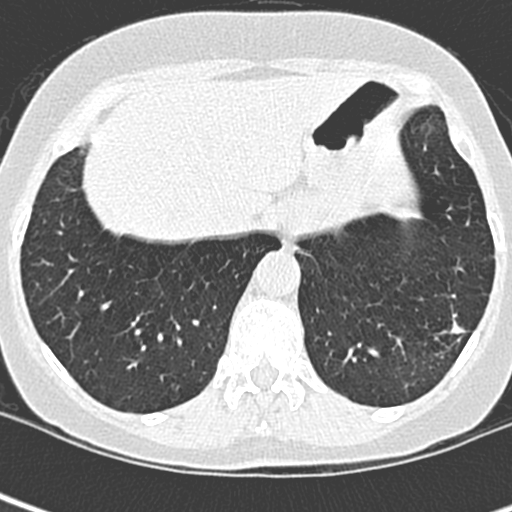
Low-dose screening chest CT, one axial slice. Position 62 of 252 along the scan axis. Lung window (W 1500 / L -600 HU). 1.3 mm slice thickness. 512 × 512 image matrix, field of view 271 × 271 mm.
Outlined on this slice (expert manual segmentation):
- lesion 1 (tumor, lower lobe of left lung): bounding box [x1, y1, x2, y2] px = [449, 319, 465, 334]